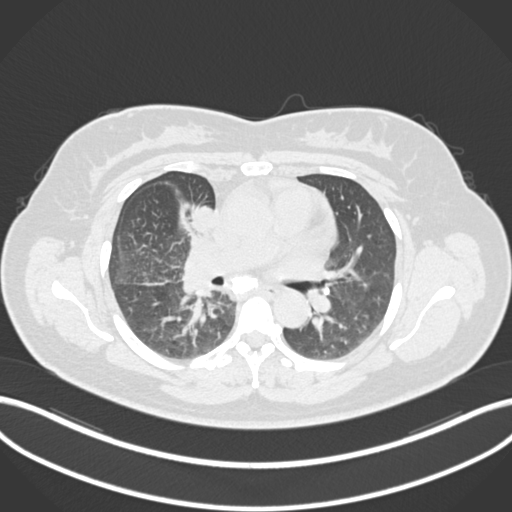
Chest CT, one axial slice; slice 97 of 183 in the series (ordered by position); 120 kVp; lung window (W 1500 / L -600 HU); 512 × 512 image matrix. Patient: female, 46 years. From the clinical record (not read from this slice): clinical TNM (as recorded): T2a N1 M0.
Outlined on this slice (rectangle marked by the reading radiologist):
- lung tumour (recorded histology: adenocarcinoma): bounding box [x1, y1, x2, y2] px = [189, 201, 225, 240]